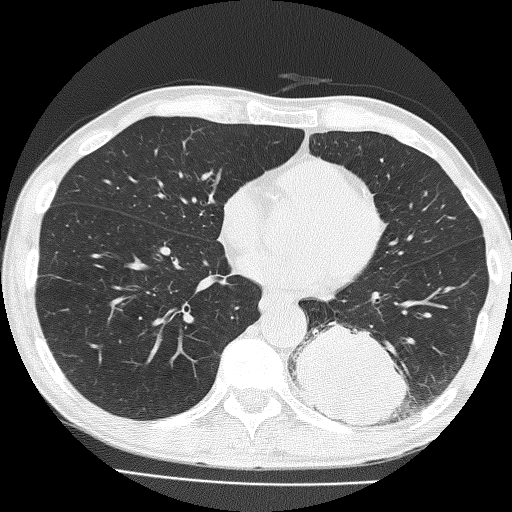
Low-dose screening chest CT, one axial slice; slice 66 of 160 in the series (ordered by position); reconstruction kernel FC51; 120 kVp; lung window (W 1500 / L -600 HU); 2 mm slice thickness; 512 × 512 image matrix, field of view 324 × 324 mm.
Structures marked on this image (expert manual segmentation):
- lesion 1 (tumor, lower lobe of left lung): bounding box (x1, y1, x2, y2) in pixels: (293, 322, 408, 426)